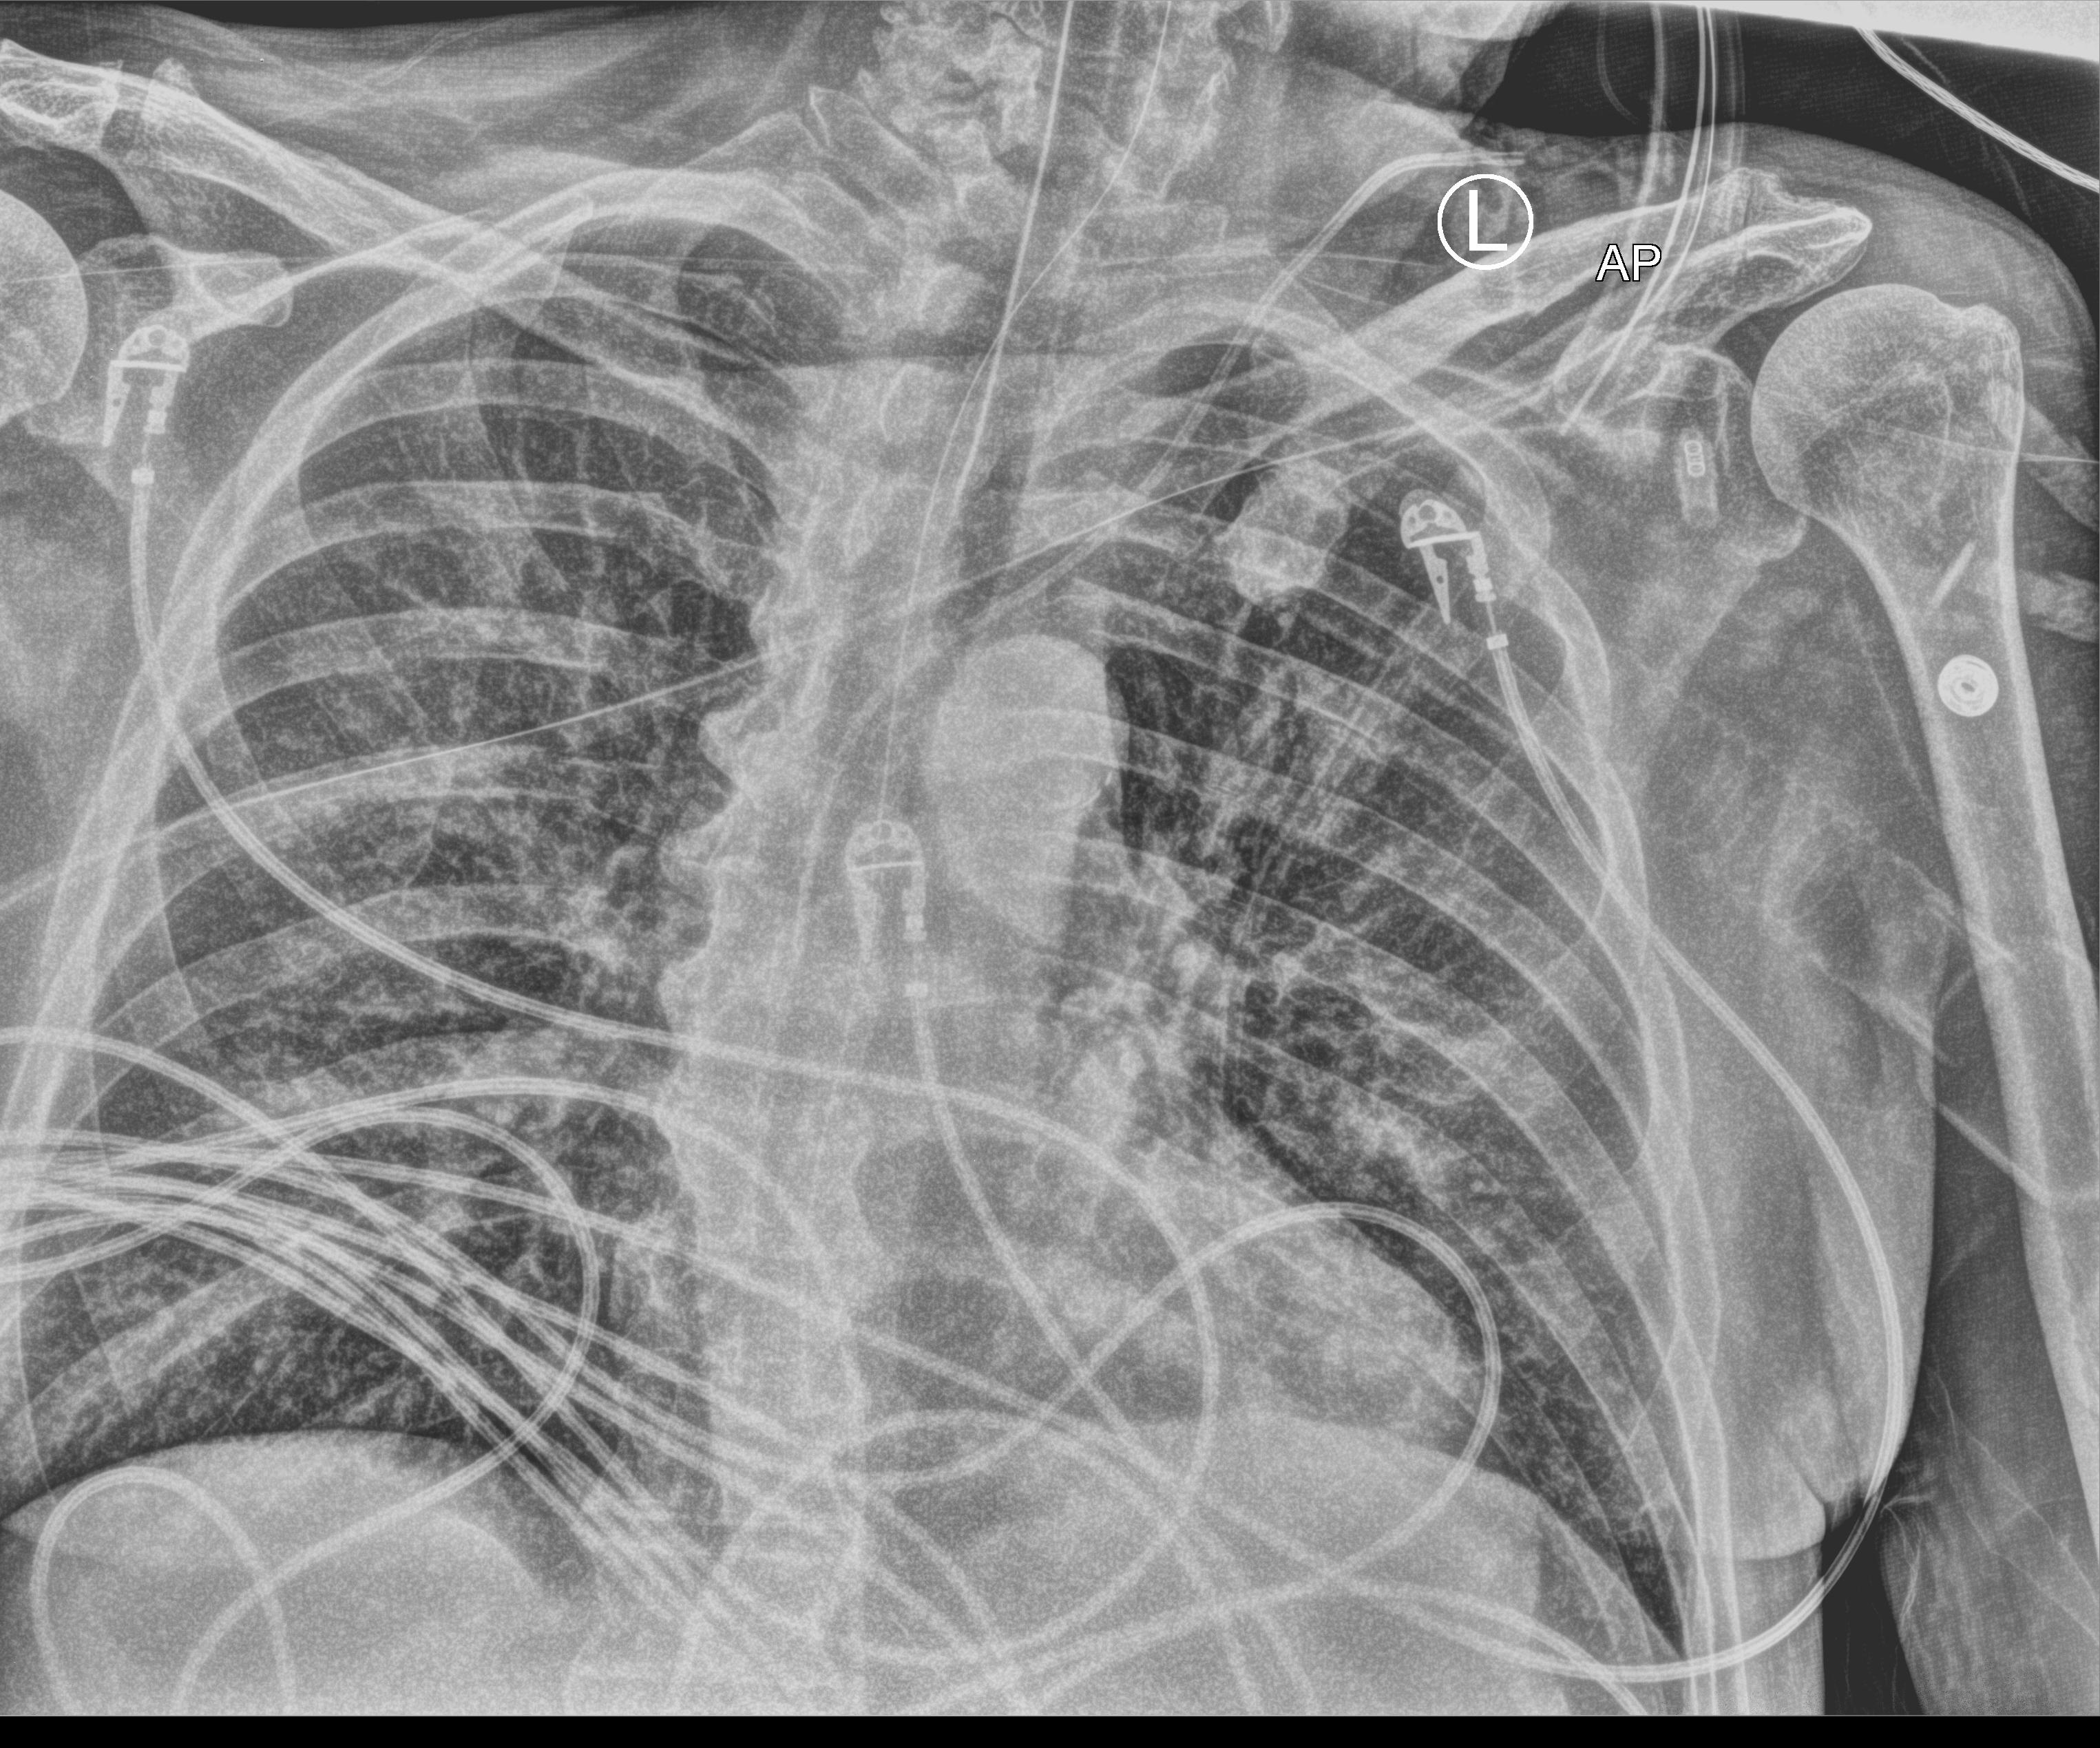
Bedside chest radiograph (computed radiography); anteroposterior (AP) projection. Male patient hospitalised with COVID-19, age 60–74 years.
From the hospital-stay record, not from the radiograph (when in the stay this image was taken is not recorded): hypertension (admission record): yes; mechanically ventilated during this hospital stay: yes; COPD (admission record): no.